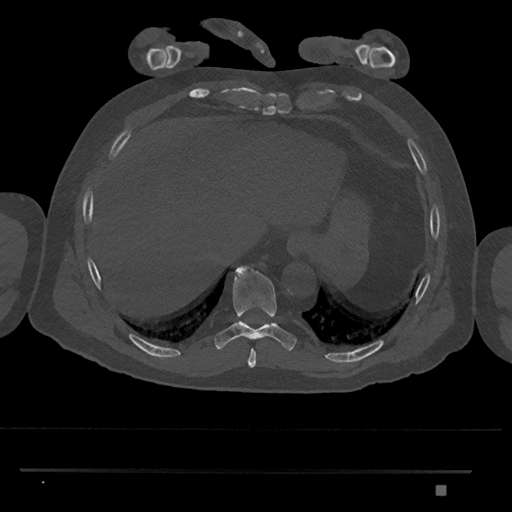
CT including the spine, one axial slice; slice 1057 of 1134 in the series (ordered by position); reconstruction kernel Br40s/3; 120 kVp; bone window (W 1800 / L 400 HU); 512 × 512 image matrix. Male patient, age 65 years. From the clinical record (not read from this slice): primary cancer: prostate.
Outlined on this slice (semi-automatic segmentation, software-assisted and operator-edited):
- T8 vertebra: bounding box [x1, y1, x2, y2] px = [247, 349, 256, 367]
- T9 vertebra: [215, 266, 298, 351]